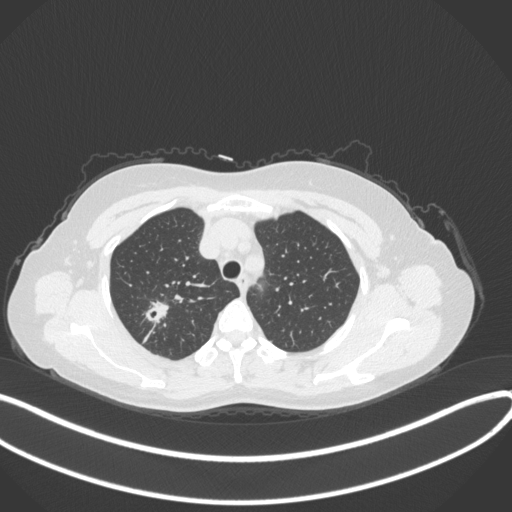
Chest CT, one axial slice. Position 289 of 342 along the scan axis. Reconstruction kernel B31f. 120 kVp. Lung window (W 1500 / L -600 HU). 1 mm slice thickness. 512 × 512 image matrix, field of view 400 × 400 mm. Female patient, age 50 years. Case-level facts recorded for this patient, not image findings: clinical TNM (as recorded): T1c N0 M0.
Structures marked on this image (bounding box drawn by a radiologist):
- lung tumour (recorded histology: adenocarcinoma): bounding box [x1, y1, x2, y2] px = [144, 297, 169, 323]